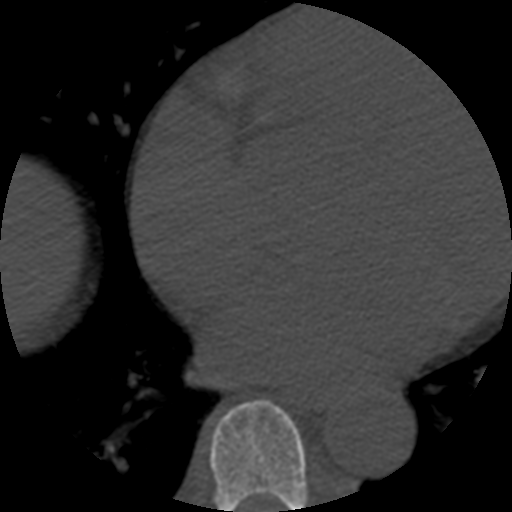
CT including the spine, one axial slice. Position 333 of 508 along the scan axis. Bone window (W 1800 / L 400 HU). 512 × 512 image matrix, field of view 160 × 160 mm. Patient age 57 years. From the clinical record (not read from this slice): primary cancer: prostate.
Annotated regions visible in this slice (semi-automatic segmentation, software-assisted and operator-edited):
- T7 vertebra: bounding box [x1, y1, x2, y2] px = [209, 400, 308, 512]